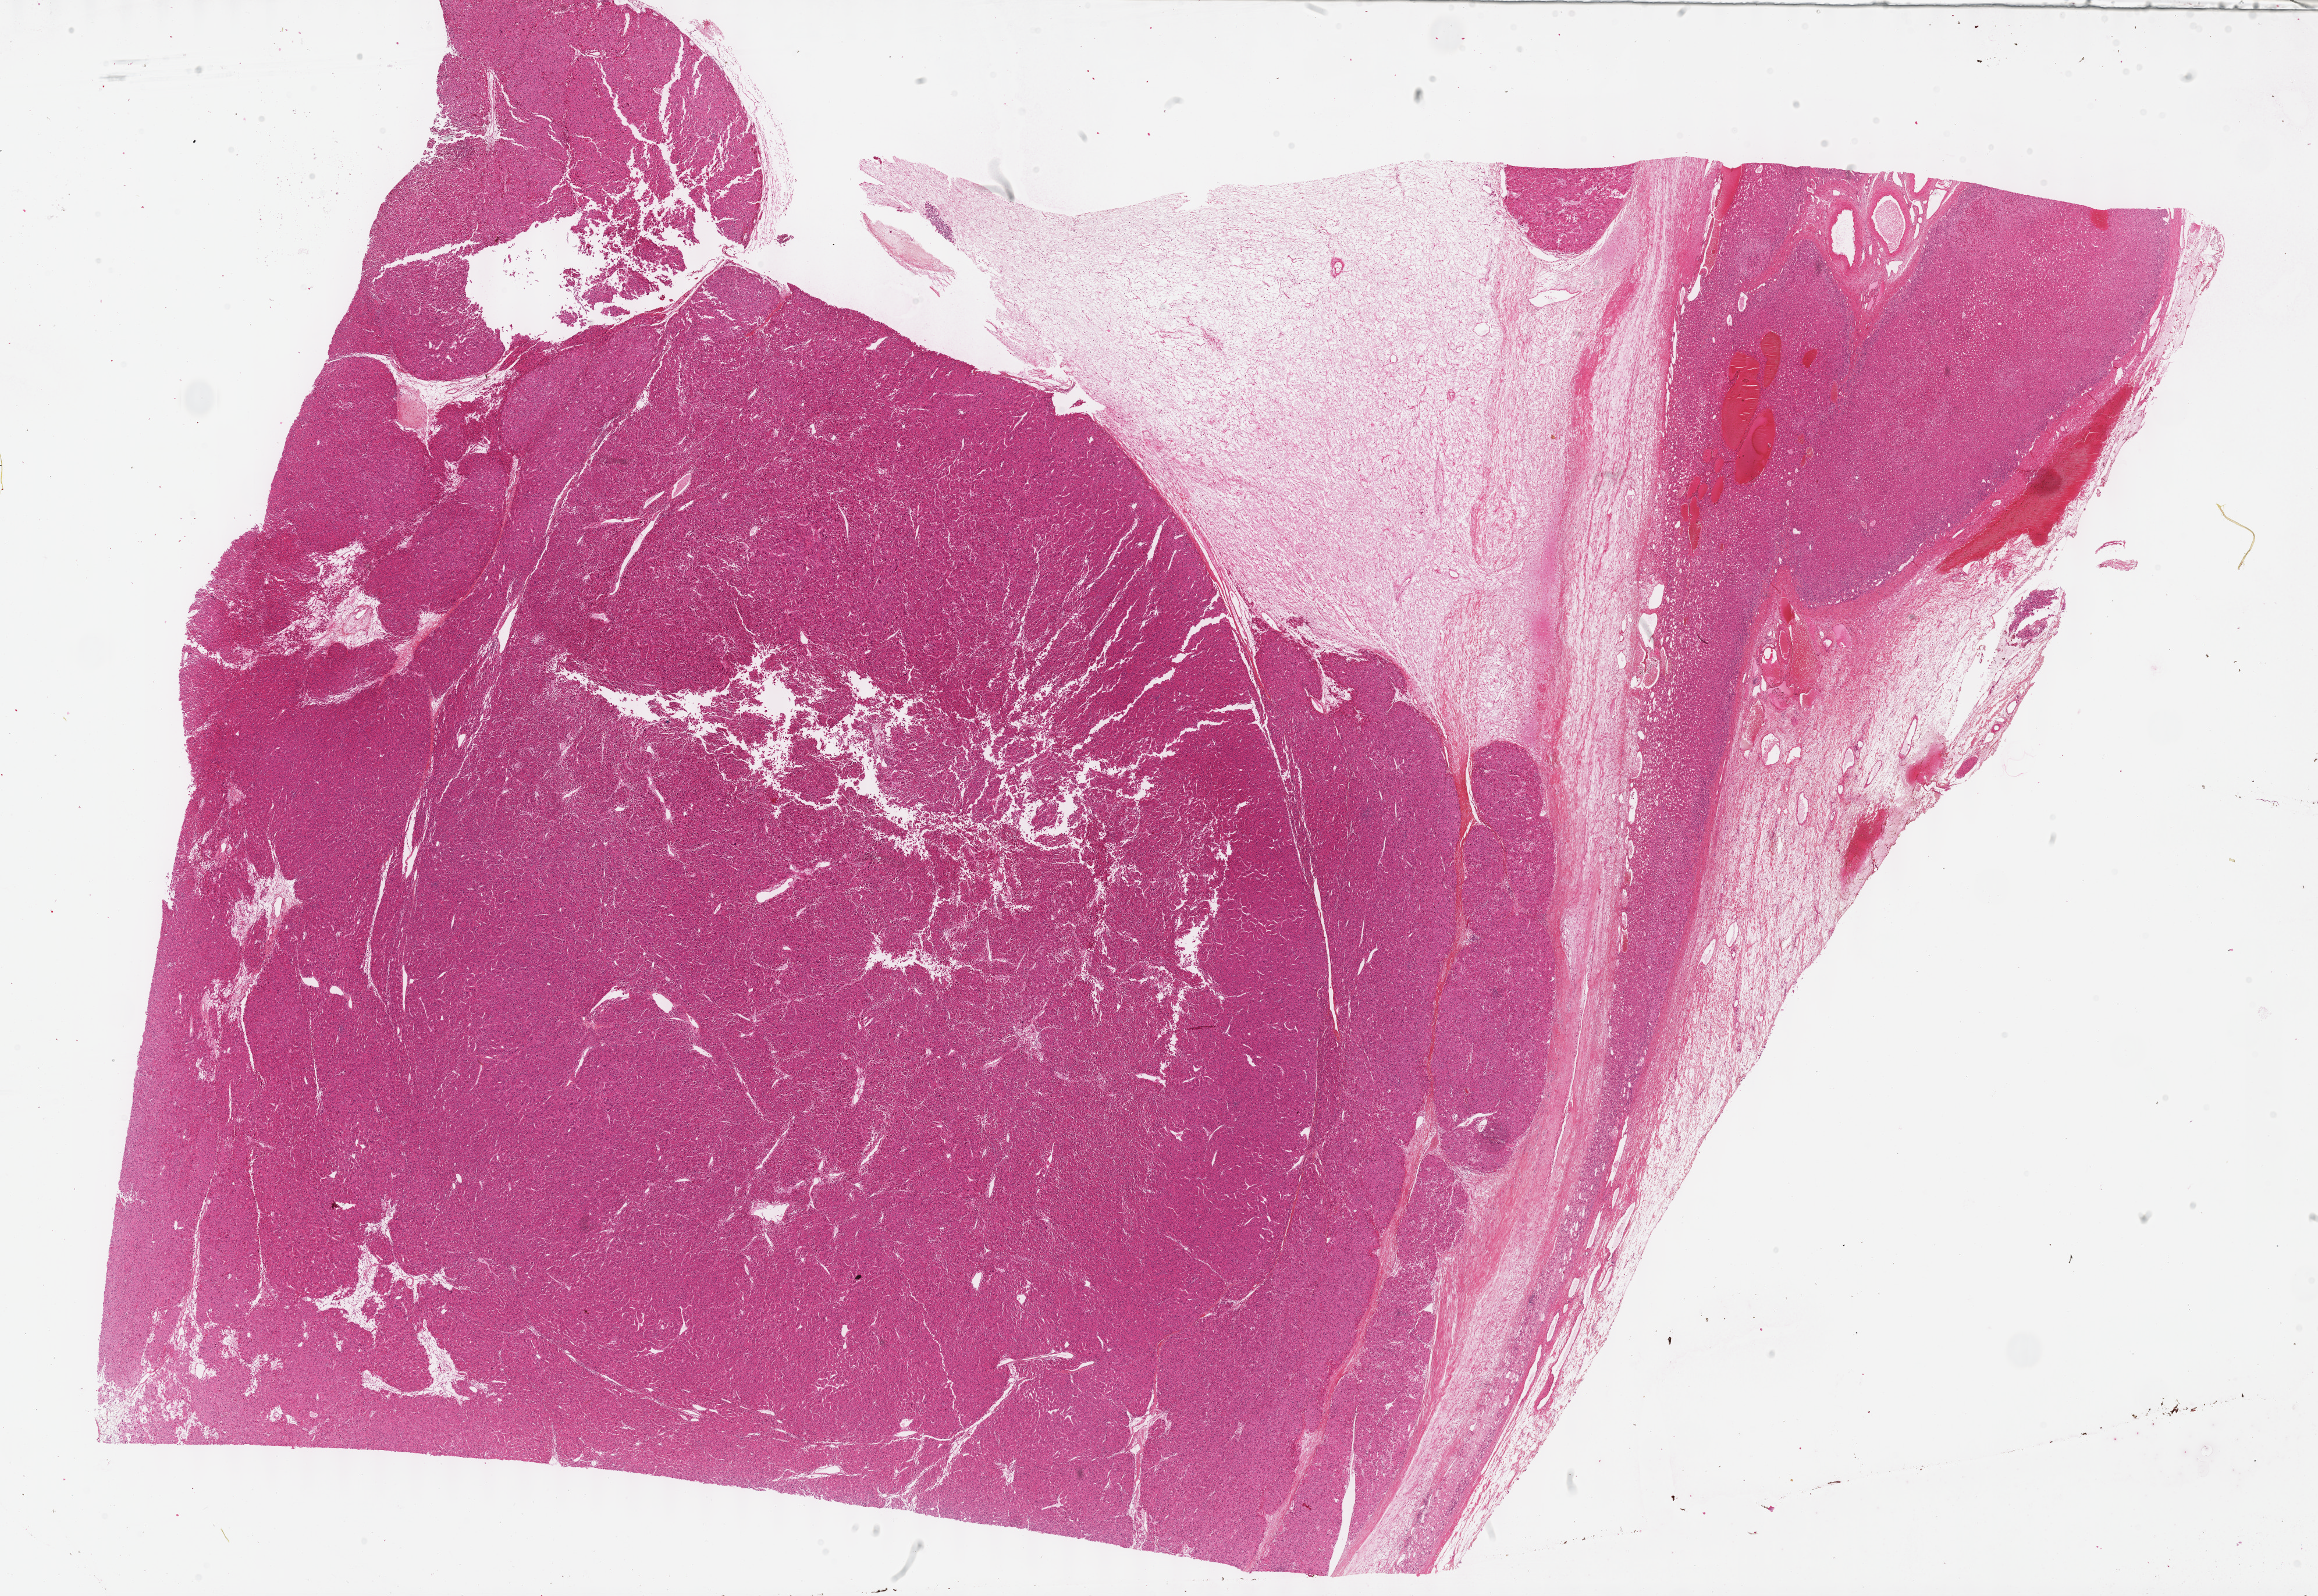
Whole-slide histology image, H&E — shown as a low-resolution overview of the whole scanned area (about 32.2 x 22.2 mm, acquisition: 40x scan). Formalin-fixed paraffin-embedded (FFPE) diagnostic section. Adrenal cortex, primary tumour sample. Female, age 31 years at initial diagnosis.
Lymph nodes positive (case pathology): 0 of 10 examined. Diagnosis: Adrenal cortical carcinoma (cortex of adrenal gland).